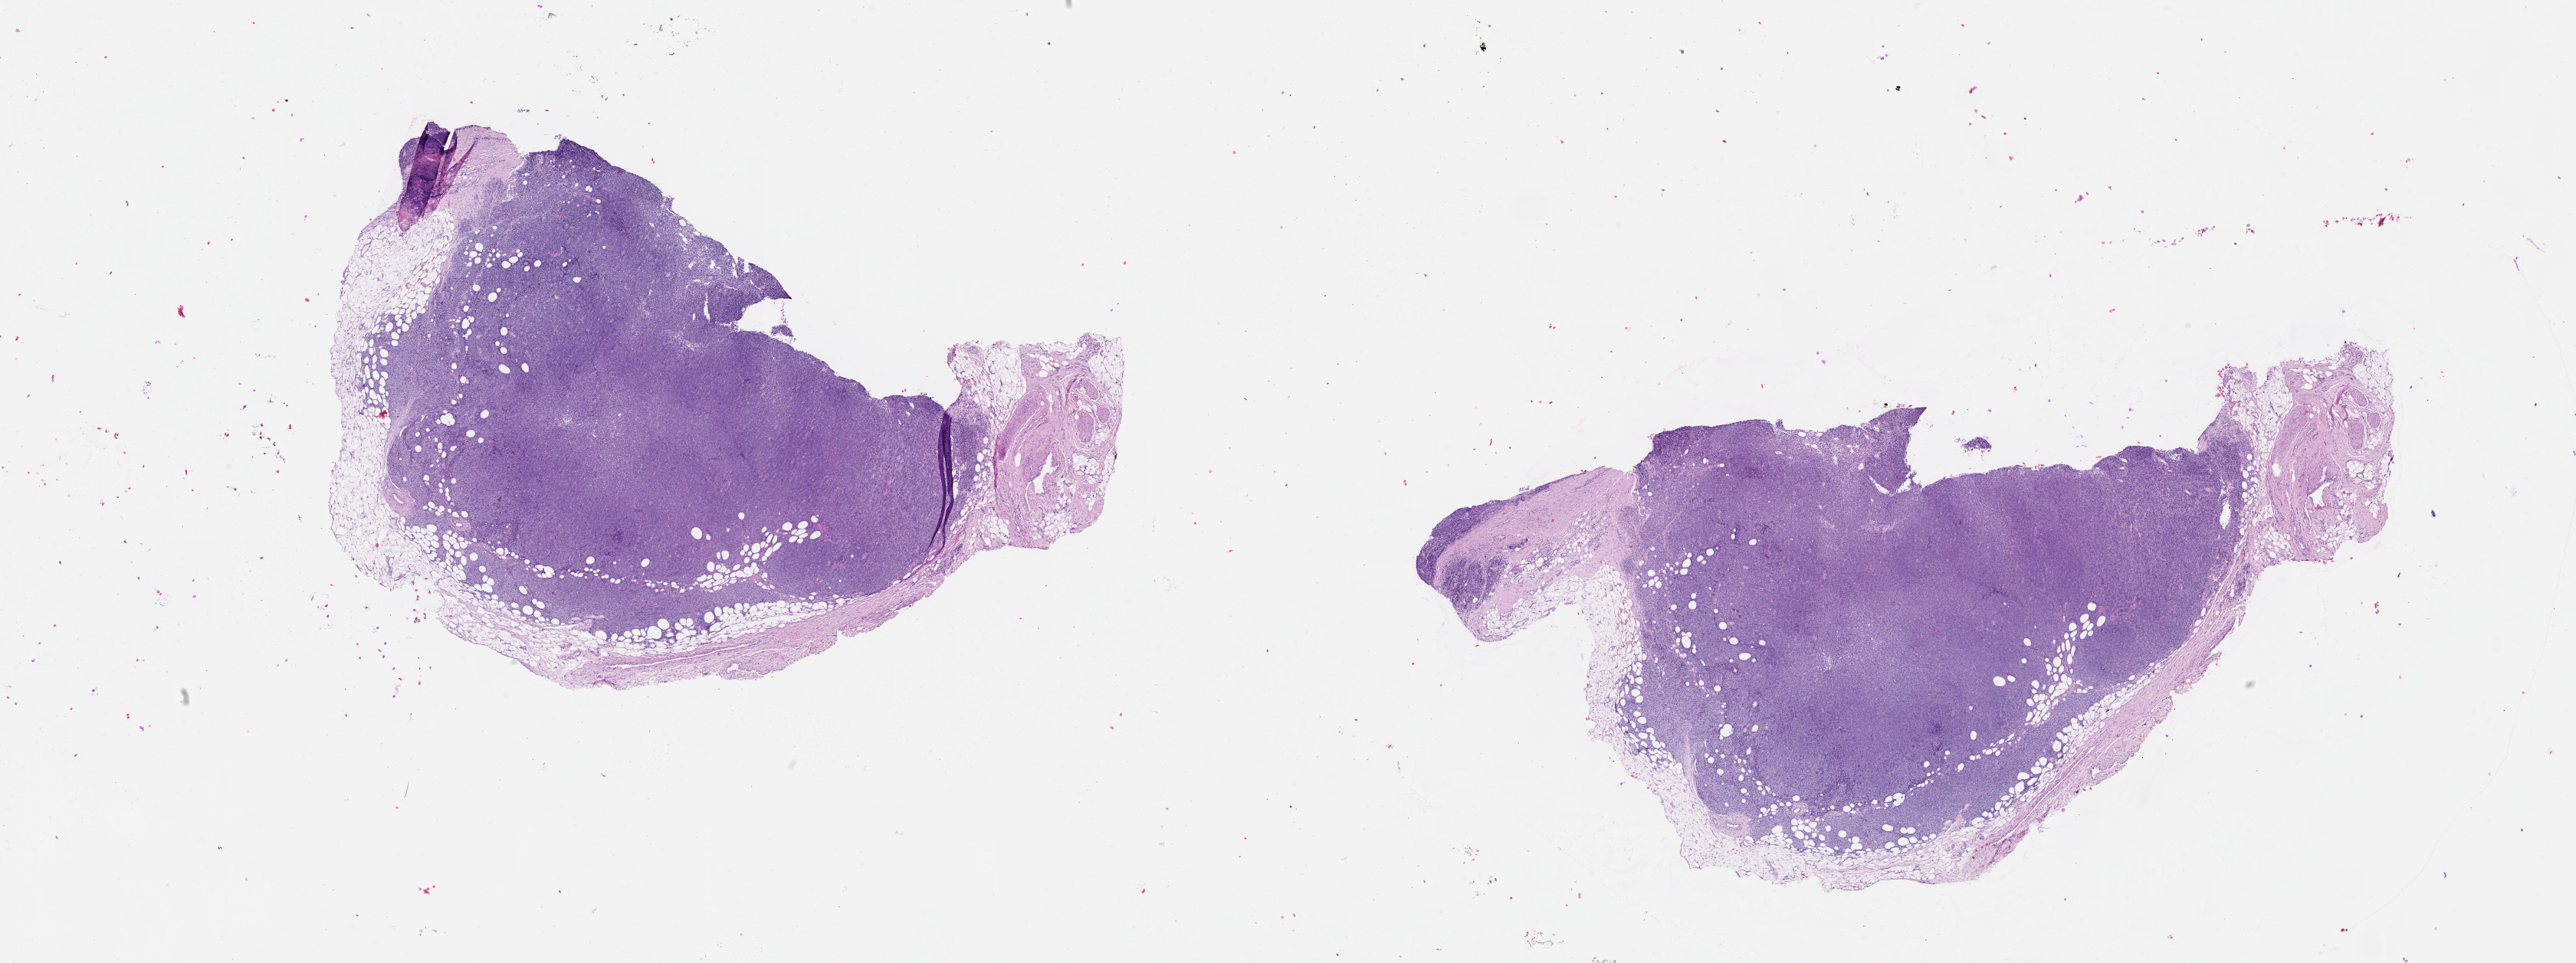
Whole-slide histology image, Hematoxylin and eosin (H&E) stained, shown as a low-resolution overview of the whole scanned area (about 27.1 x 10.1 mm). 72-year-old male patient.
Patient diagnosis: Malignant melanoma, NOS.